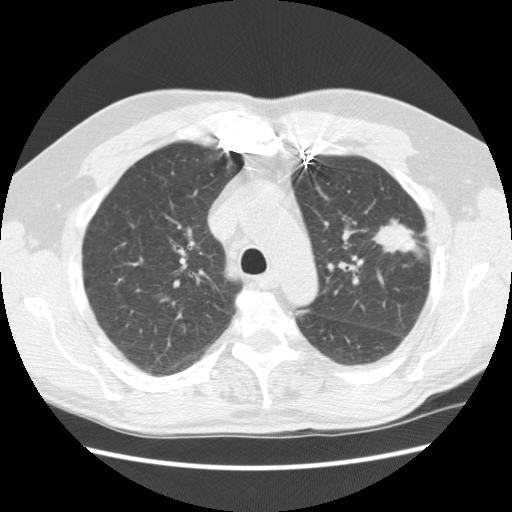
Chest CT (low-dose screening protocol), one axial image. Baseline annual screen. Lung window (W 1500 / L -600 HU). 2.5 mm slice thickness. Slice 174 of 231 in the series. Male, age 72 years at enrolment. Former smoker at enrolment.
Expert-annotated lung lesion, bounding box <351,201,428,259> (left, top, right, bottom; pixels). The exam's reader record, not a measurement of the box and not confirmed to be the same lesion: non-calcified nodule or mass ≥4 mm, left upper lobe, 25 × 18 mm, spiculated (stellate) margins, soft tissue attenuation. Participant outcome: lung cancer diagnosed 35 days after this screen — adenocarcinoma, NOS, left upper lobe, well differentiated (G1), stage IIIB (AJCC 6th edition), 25 mm at pathology.